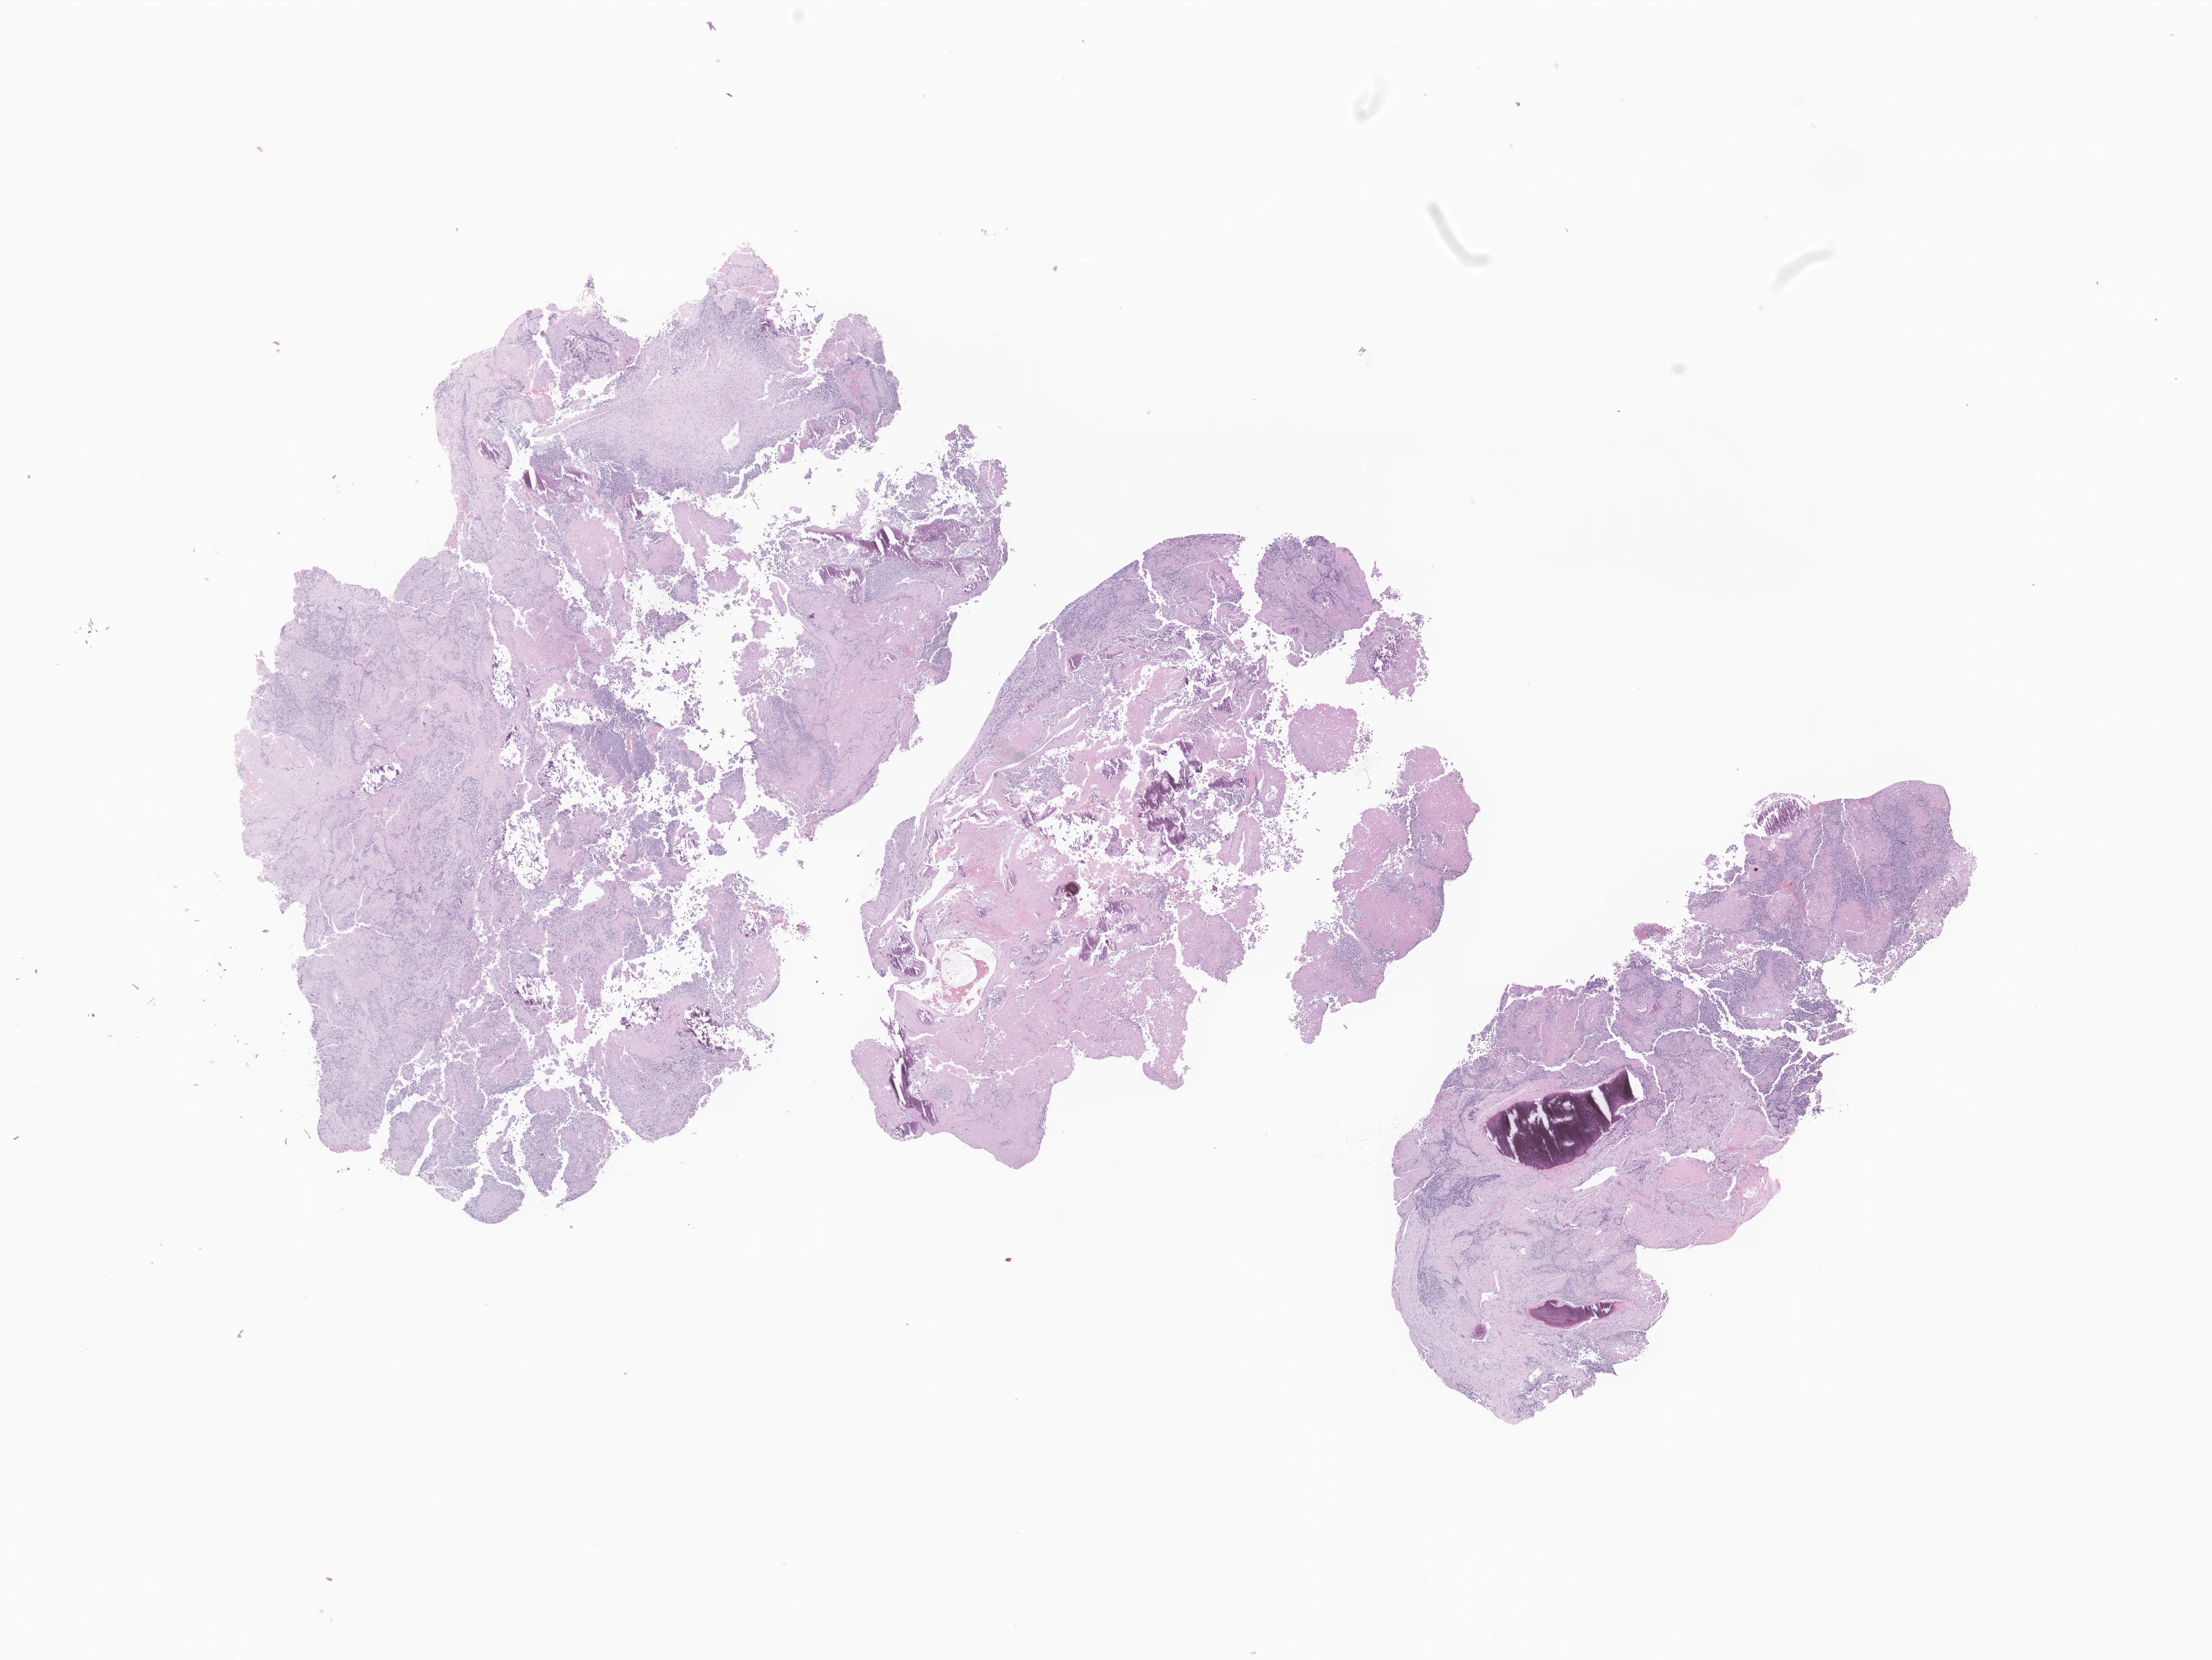
Digitized hematoxylin and eosin (H&E)-stained section of tumor tissue from the lower limb — whole scanned area (about 17.2 x 12.9 mm) shown as a low-resolution overview. Formalin-fixed, paraffin-embedded (FFPE) tissue. Male patient, age 157 months (13 years 1 month).
* recorded diagnosis: Neoplasm, malignant